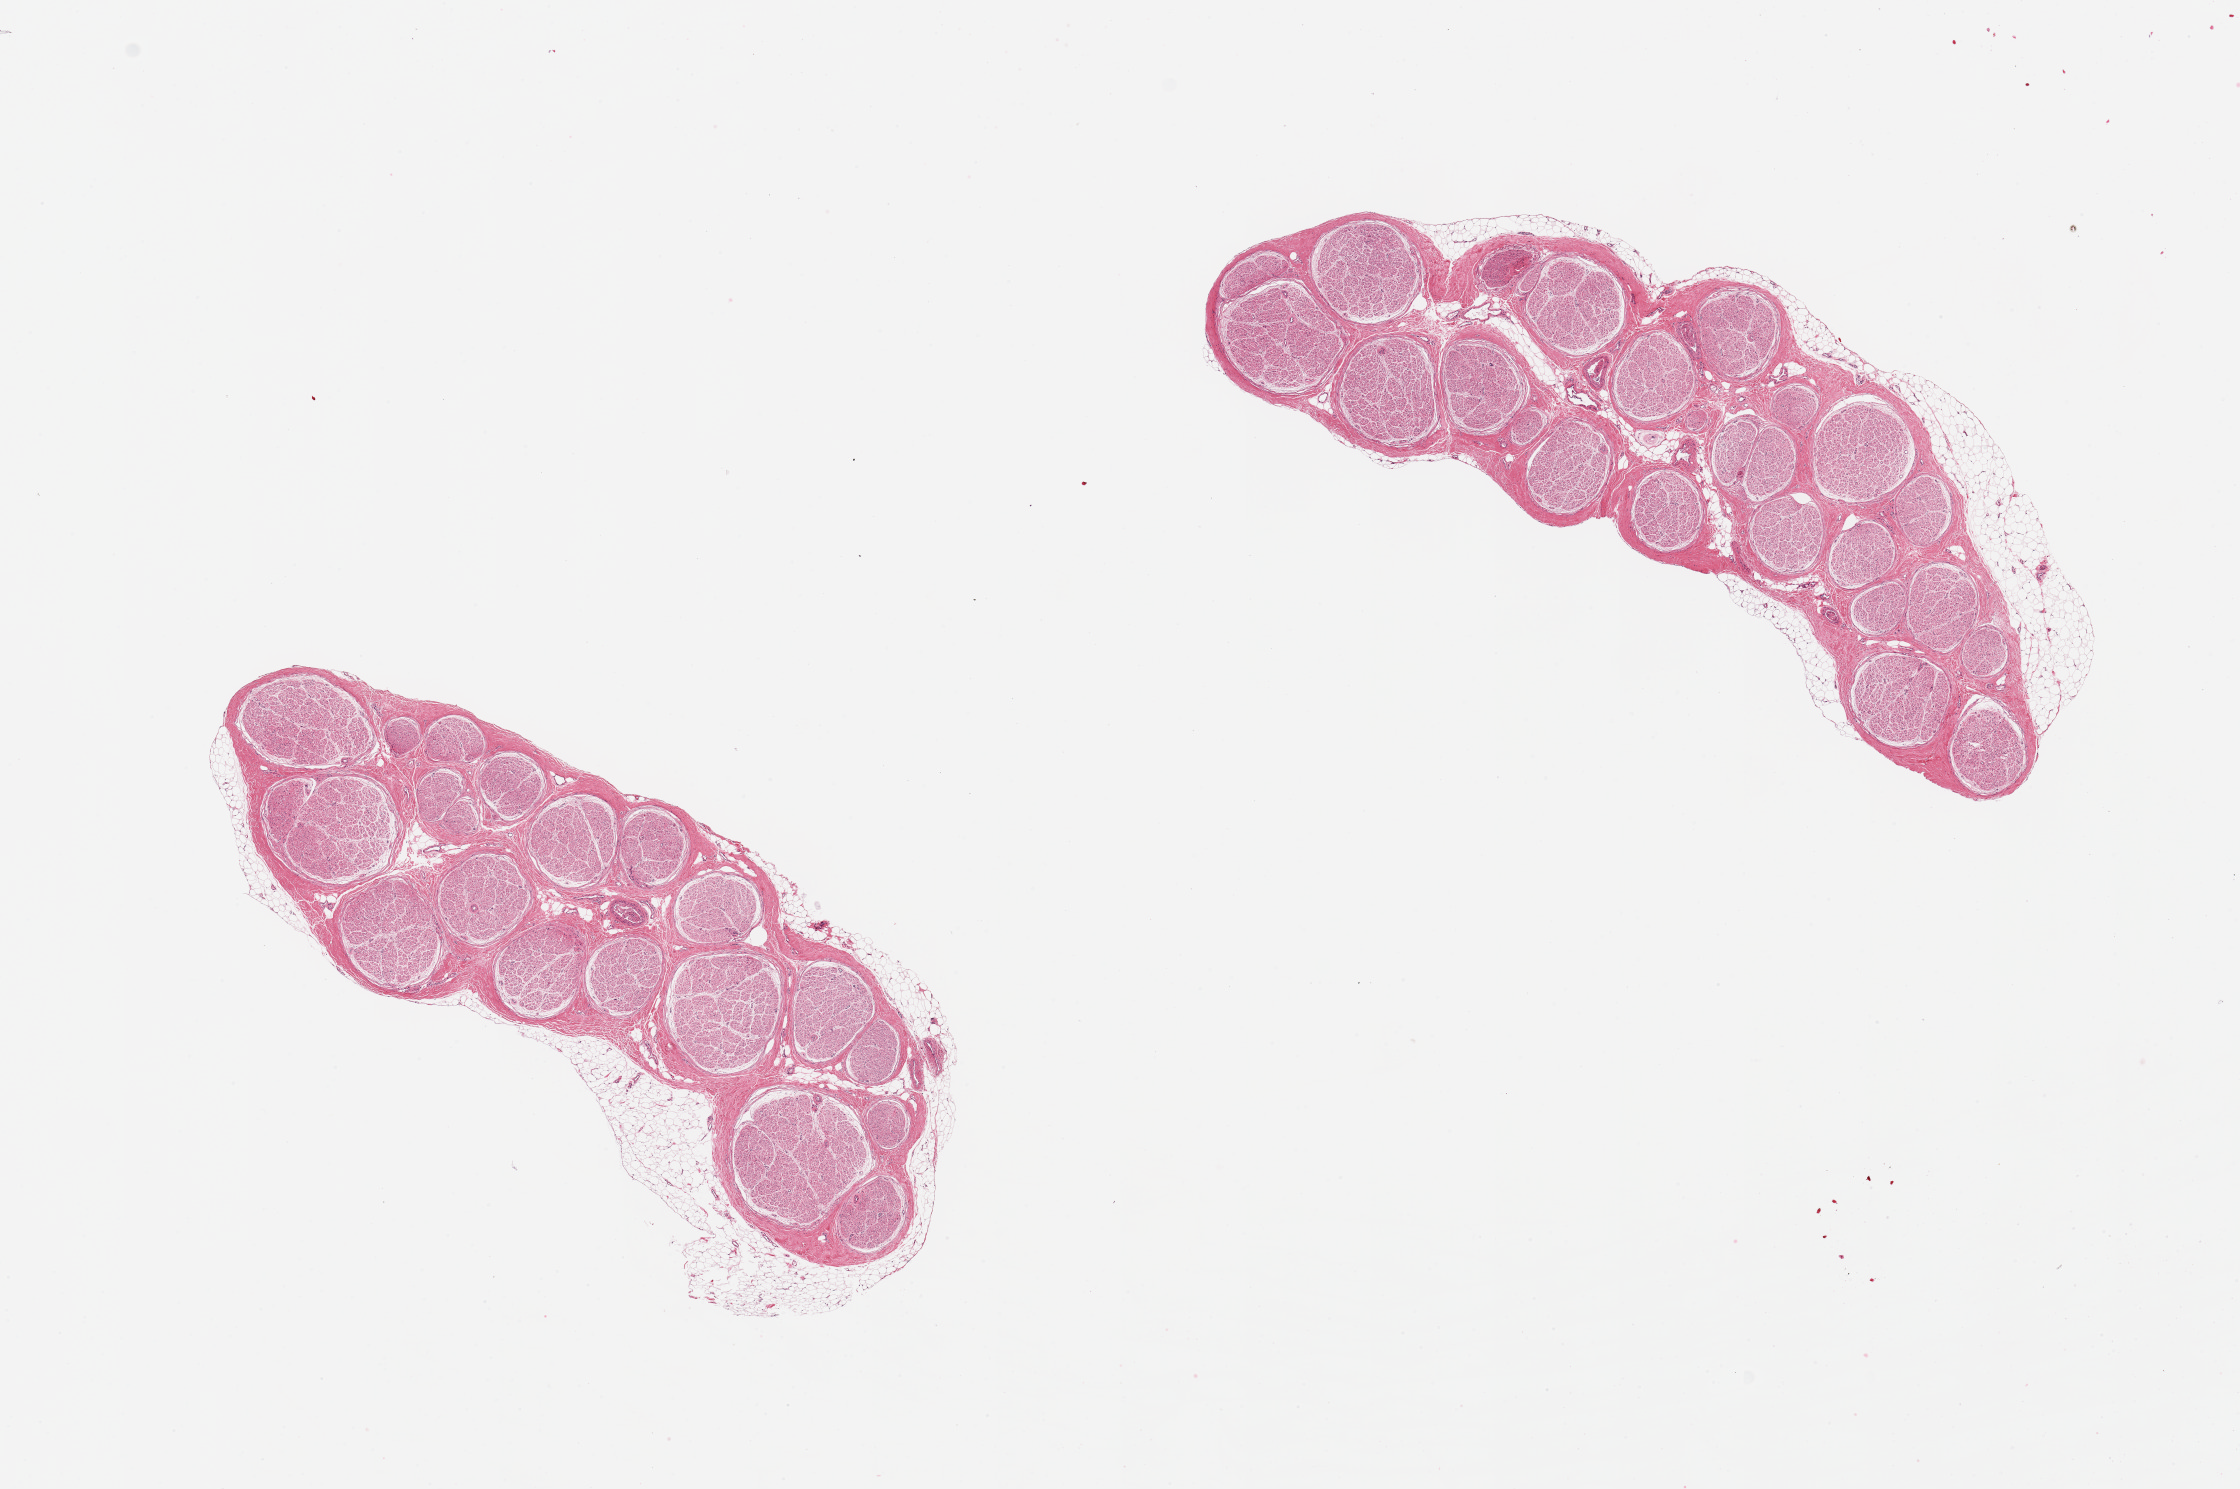
Whole-slide image, H&E stain, brightfield, shown as a low-resolution overview of the whole scanned area (about 17.7 x 11.8 mm). PAXgene-fixed, paraffin-embedded tissue. Sampled site (target tissue): tibial nerve. Tissue donor sample. Donor sex: male.
Reviewer comment on this tissue sample: 2 pieces, trace adherent fat up to ~0.5mm.